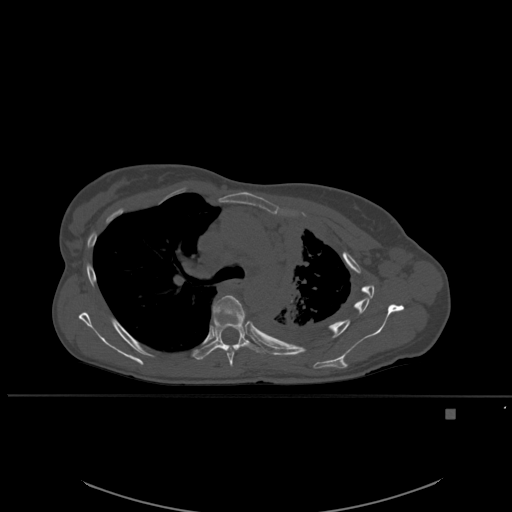
CT including the spine, one axial slice; position 390 of 537 along the scan axis; bone window (W 1800 / L 400 HU); 1.5 mm slice thickness; 512 × 512 image matrix, field of view 440 × 440 mm. Female patient, age 45 years. Case-level facts recorded for this patient, not image findings: primary cancer: lung.
Annotated regions visible in this slice (semi-automatically segmented with operator editing):
- T5 vertebra: bounding box (x1, y1, x2, y2) in pixels: (213, 295, 246, 367)
- T6 vertebra: (196, 317, 268, 361)